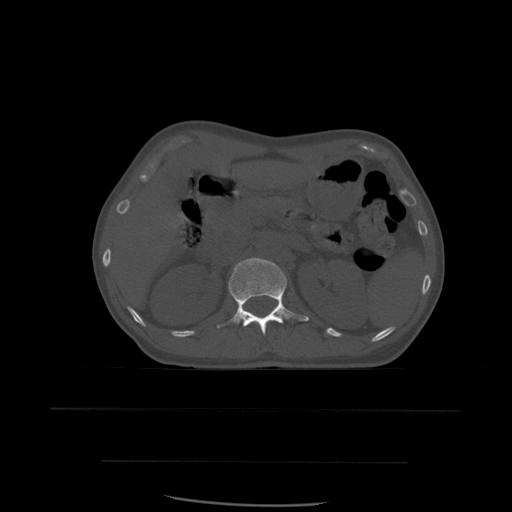
CT including the spine, one axial slice. Position 249 of 574 along the scan axis. Bone window (W 1800 / L 400 HU). 1.25 mm slice thickness. 512 × 512 image matrix. Patient age 48 years. From the clinical record (not read from this slice): primary cancer: lung.
Annotated regions visible in this slice (semi-automatically segmented with operator editing):
- L1 vertebra: bounding box (x1, y1, x2, y2) in pixels: (217, 258, 309, 335)